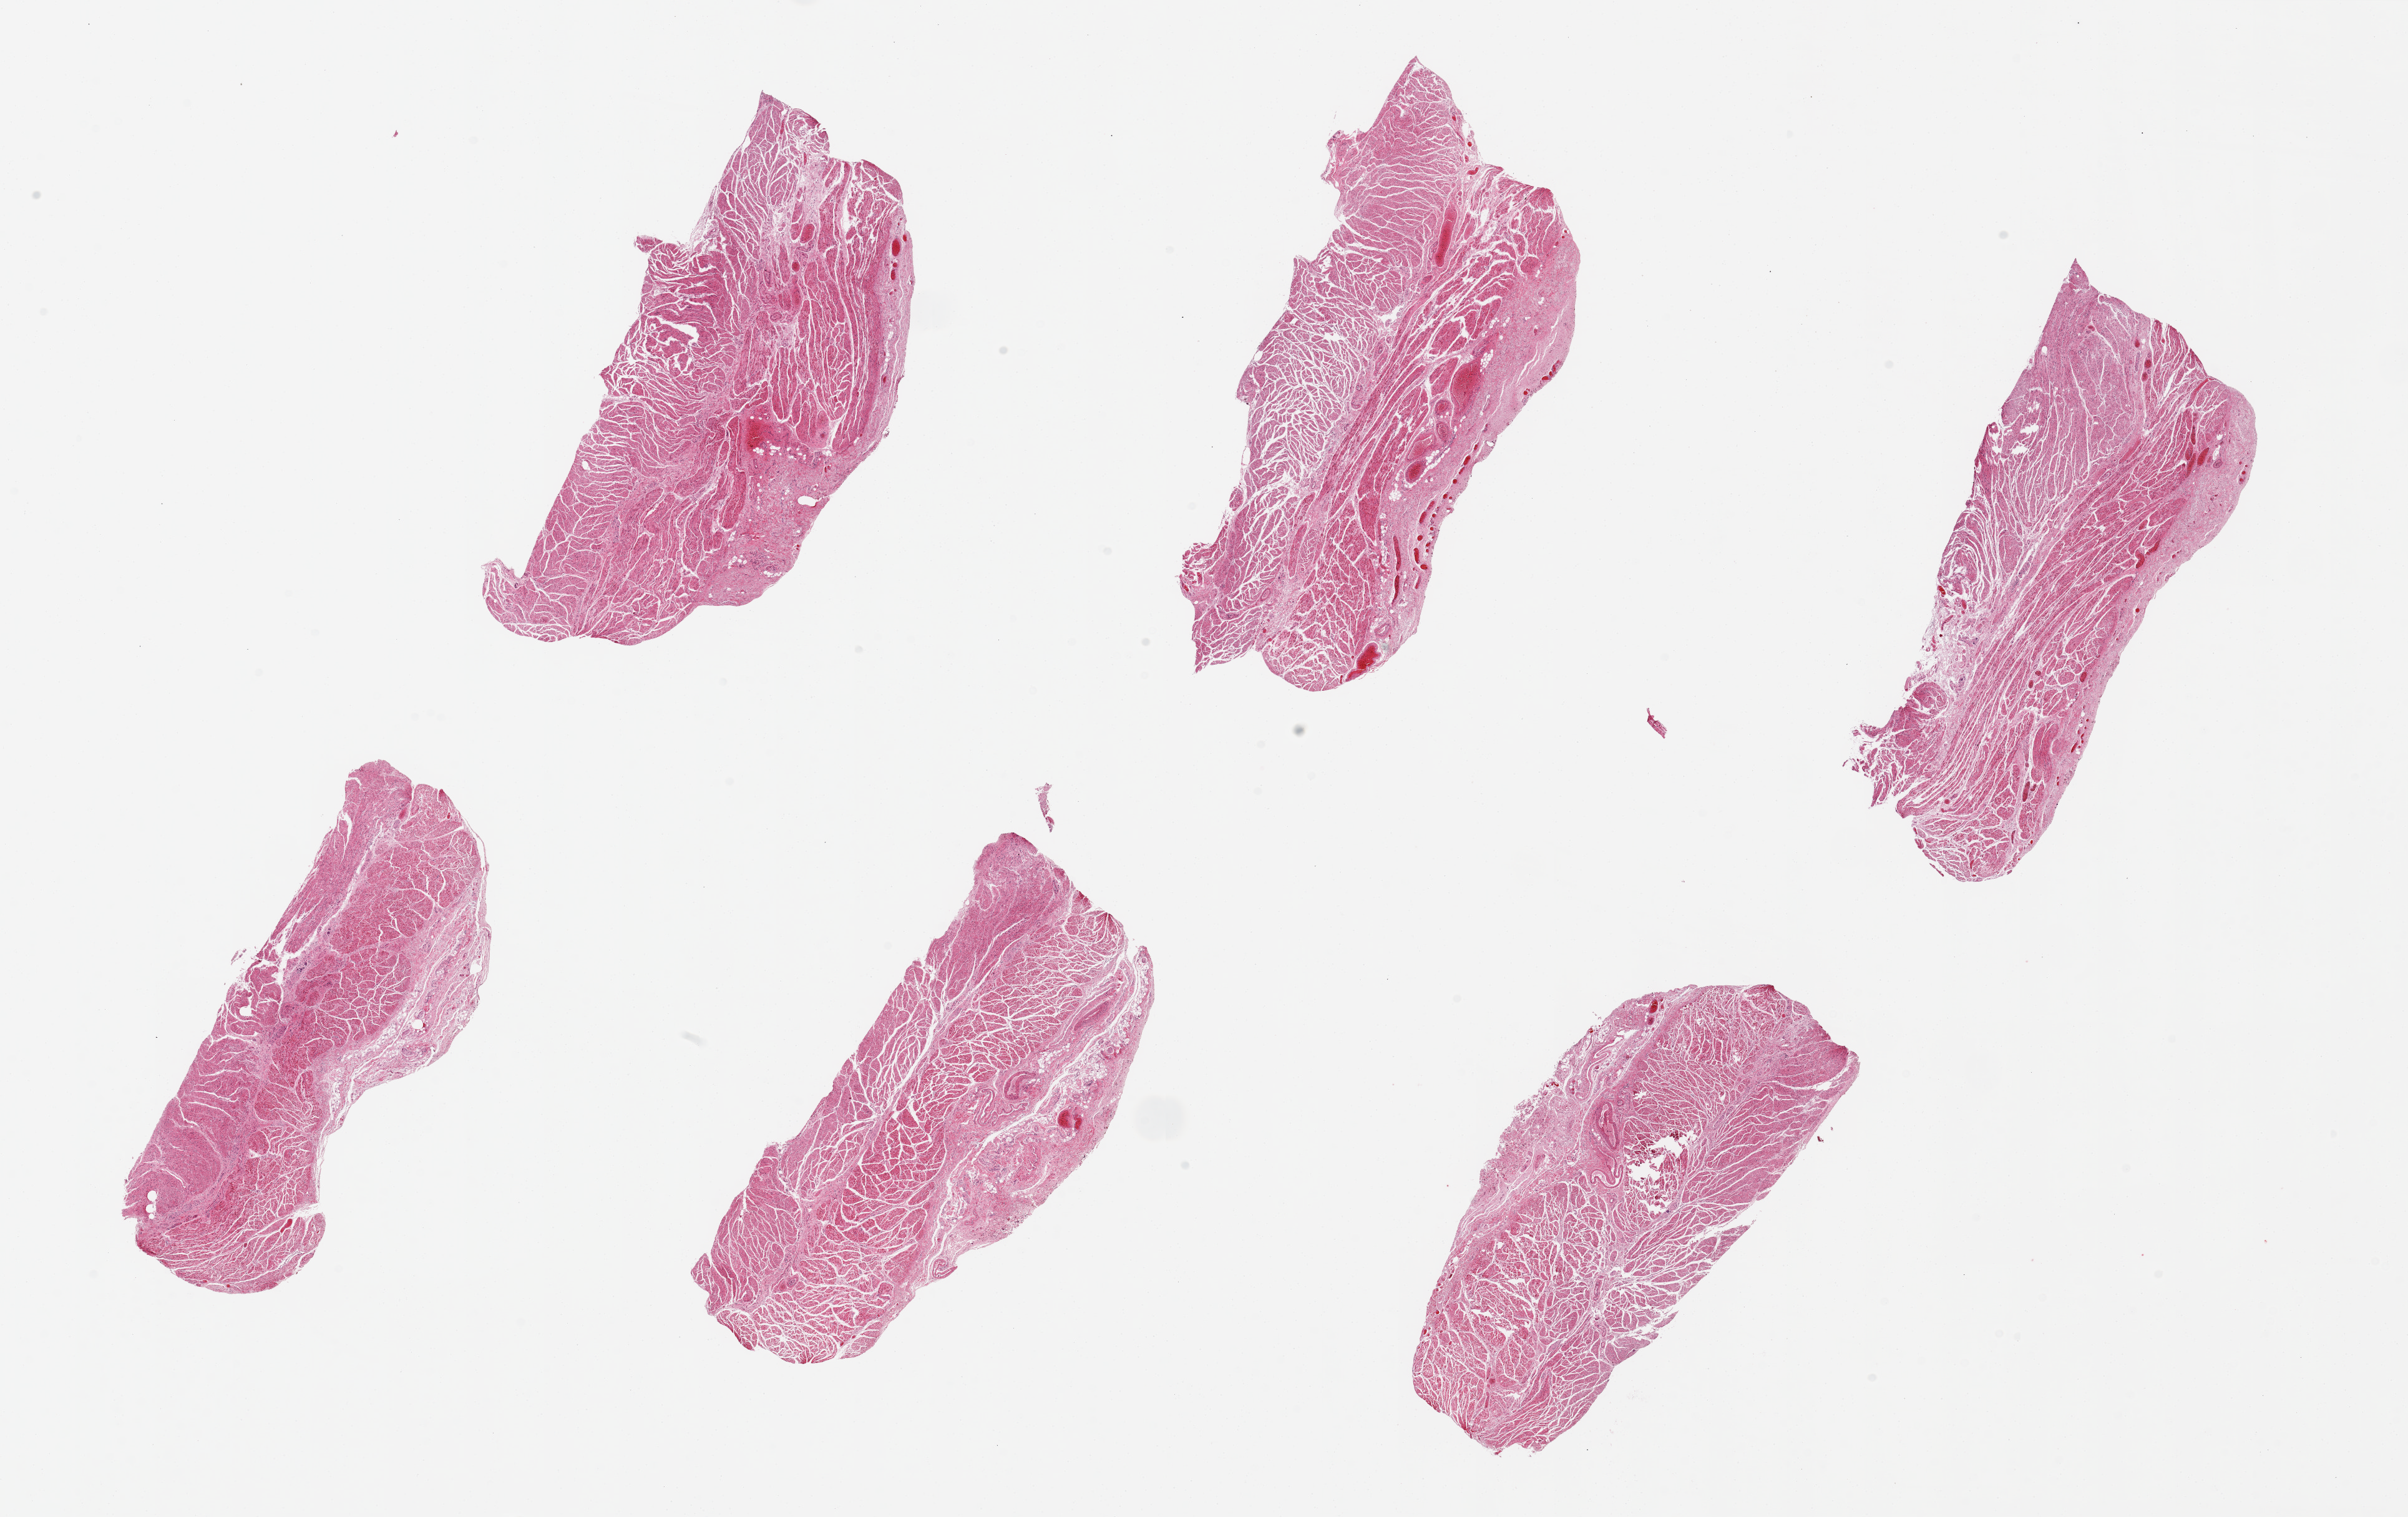
Digitized hematoxylin and eosin (H&E)-stained section — whole scanned area (about 30.5 x 19.2 mm) shown as a low-resolution overview. PAXgene-fixed paraffin-embedded (PFPE) section. Sampled site (target tissue): gastroesophageal junction. Tissue donor sample. Donor sex: male.
Pathologist's review note for this sample: 6 pieces up to 8x4mm; muscle more poorly preserved than usual.